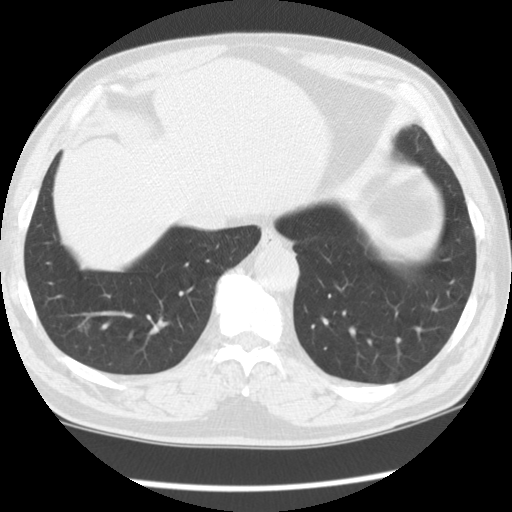
Low-dose screening chest CT, axial slice, baseline annual screen, lung window (W 1500 / L -600 HU), 2.5 mm slice thickness, standard (soft-tissue) reconstruction kernel (STANDARD). Male, age 62 years at enrolment. Former smoker at enrolment.
- Expert reader's lesion annotation, bounding box <52,296,112,357> (left, top, right, bottom; pixels).
- Screening reader's record for this exam (one nodule recorded; not confirmed to be the boxed lesion): non-calcified nodule or mass ≥4 mm, right lower lobe, 13 × 11 mm, smooth margins, ground glass attenuation.
- Official screen result: positive, change unspecified: nodule(s) >= 4 mm or enlarging nodule(s), mass(es), or other non-specific abnormalities suspicious for lung cancer.
- Lung cancer was diagnosed 874 days after this screen: bronchiolo-alveolar carcinoma, non-mucinous, right lower lobe, well differentiated (G1), stage IA (AJCC 6th edition), 14 mm at pathology.